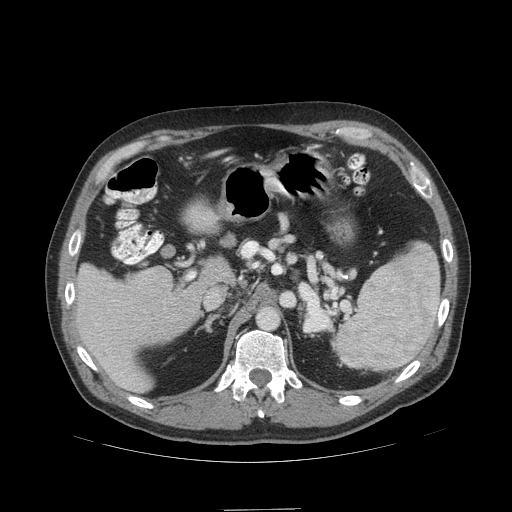
Contrast-enhanced abdominal CT (liver protocol), one axial slice; position 64 of 99 along the scan axis; reconstruction kernel STANDARD; 140 kVp; soft-tissue window (W 400 / L 40 HU); 2.5 mm slice thickness; 512 × 512 image matrix. From the clinical record (not read from this slice): diagnosis: hepatocellular carcinoma (patient treated with transarterial chemoembolisation; whether this scan precedes or follows treatment is not stated here); TNM stage (as recorded): Stage-I; Child-Pugh class: A; tumour differentiation: no biopsy.
Annotated regions visible in this slice (semi-automatic segmentation, software-assisted and operator-edited):
- liver parenchyma outside the tumour (the mass and vessels are separate outlines, so this box may not span the whole liver): bounding box <70,262,202,392> (left, top, right, bottom; pixels)
- liver vessels: <71,288,122,376>